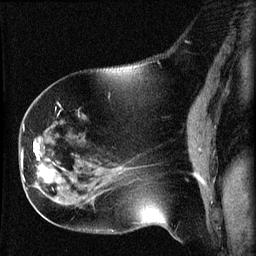
Breast MRI (dynamic contrast-enhanced), one sagittal slice. Slice 25 of 60 in the series (ordered by position). Dynamic contrast-enhanced series, image 2 of 3 at this slice position (ordered by acquisition). 1.5 T. TE 4.2 ms, TR 8.2 ms. 2 mm slice thickness. 256 × 256 image matrix, field of view 180 × 180 mm. Patient: female, 63 years.
Outlined on this slice (semi-automatic segmentation, software-assisted and operator-edited):
- analysis volume of interest (the breast-tissue region the enhancement analysis was run in; not a lesion): bounding box <22,156,64,202> (left, top, right, bottom; pixels)
- tumour enhancement mask (voxels above the 70 % enhancement threshold inside the analysis volume of interest): <22,156,64,182>